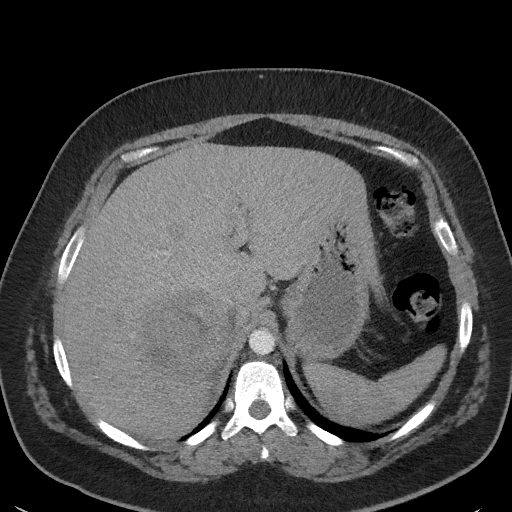
Contrast-enhanced abdominal CT, one axial slice. Position 40 of 56 along the scan axis. Reconstruction kernel I41f/3. 120 kVp. Intravenous contrast given. Soft-tissue window (W 400 / L 40 HU). 5 mm slice thickness. 512 × 512 image matrix. Female patient, age 35 years. Case-level facts recorded for this patient, not image findings: diagnosis: adrenocortical carcinoma; tumour side: right adrenal; tumour size at pathology: 15 cm; Ki-67 index: 40 %; stage (as recorded): 2.
Annotated regions visible in this slice (semi-automatic segmentation, software-assisted and operator-edited):
- mass: box from (x=145, y=291) to (x=233, y=374) px